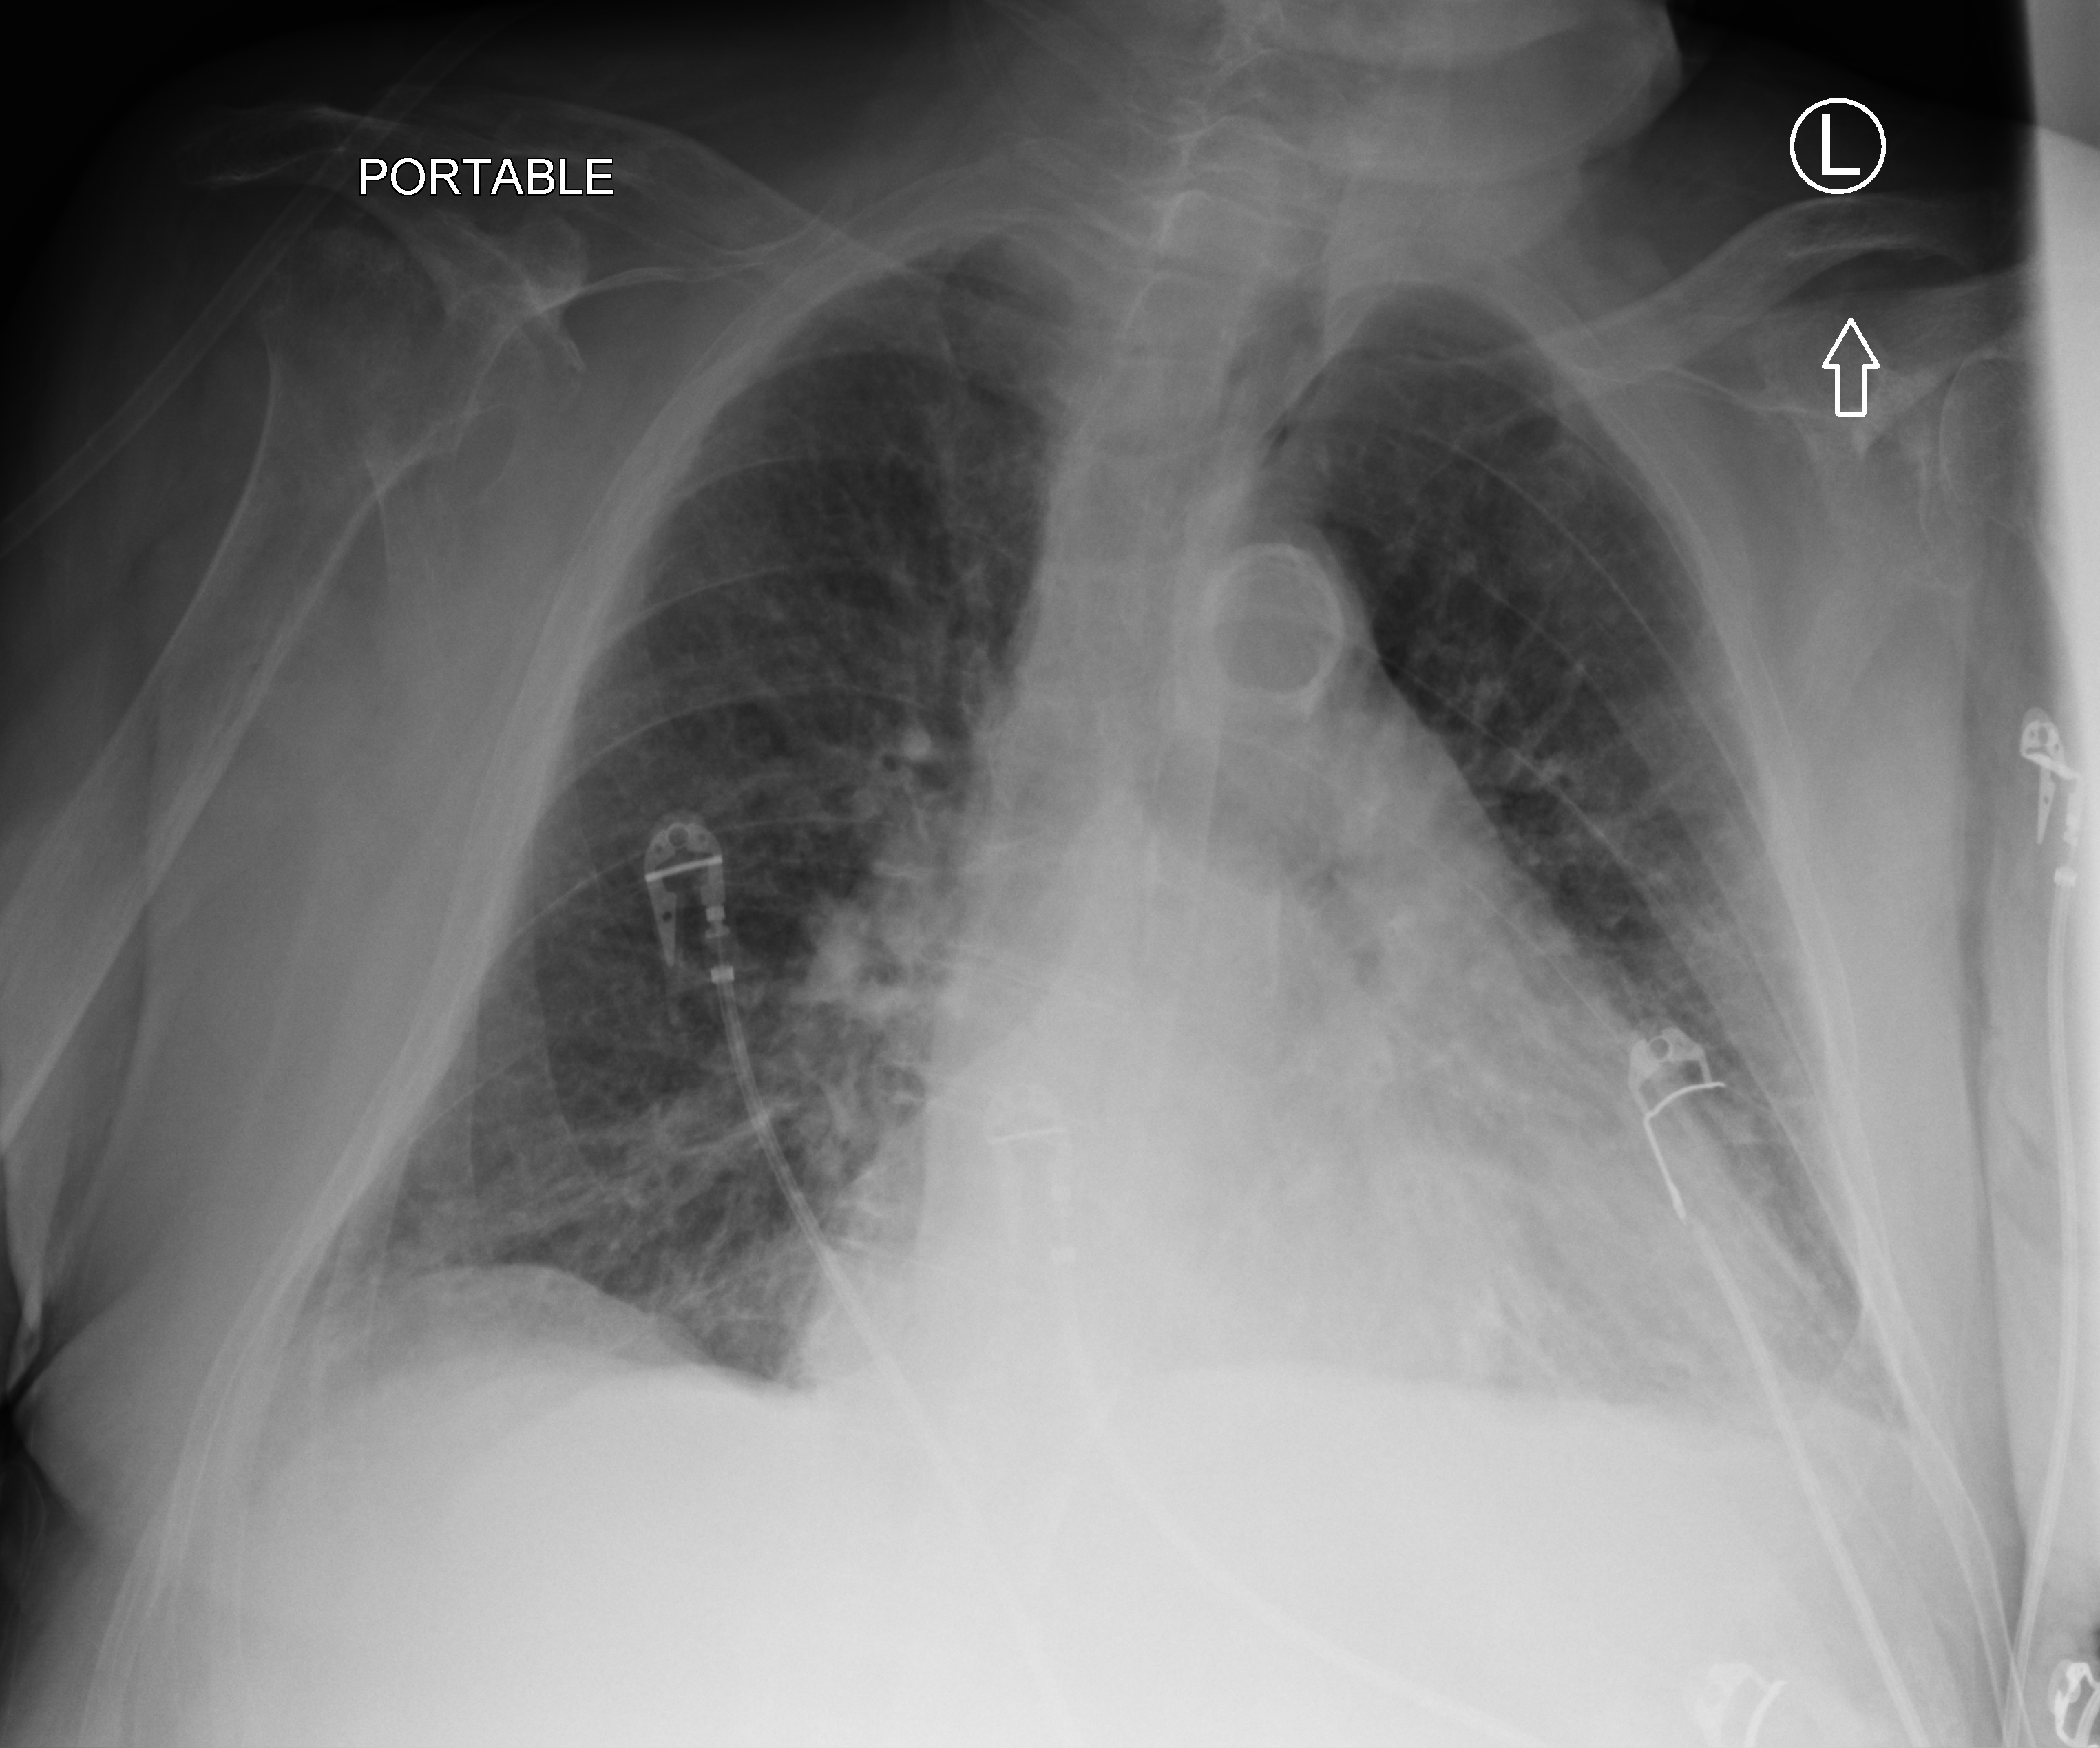
Chest X-ray (portable). Male patient hospitalised with COVID-19, age 75–90 years.
Admission-level facts for this patient (not findings on this image; timing relative to this image not recorded):
- mechanically ventilated during this hospital stay: no
- hypertension (admission record): yes
- COPD (admission record): no